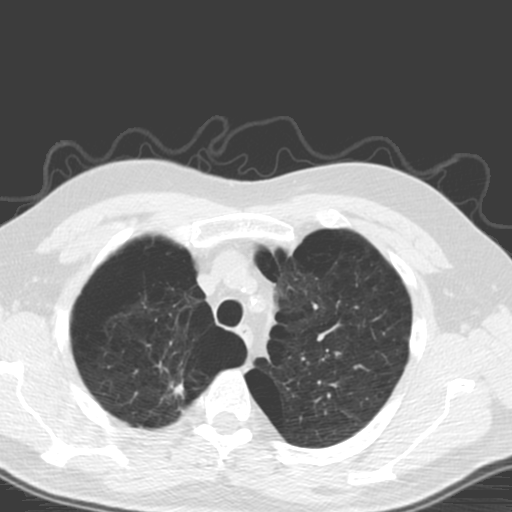
Low-dose screening chest CT, one axial slice; position 139 of 173 along the scan axis; 120 kVp; lung window (W 1500 / L -600 HU); 3.2 mm slice thickness; 512 × 512 image matrix.
Structures marked on this image (manually delineated by an expert):
- lesion 1 (tumor, upper lobe of right lung): bounding box <174,382,184,398> (left, top, right, bottom; pixels)